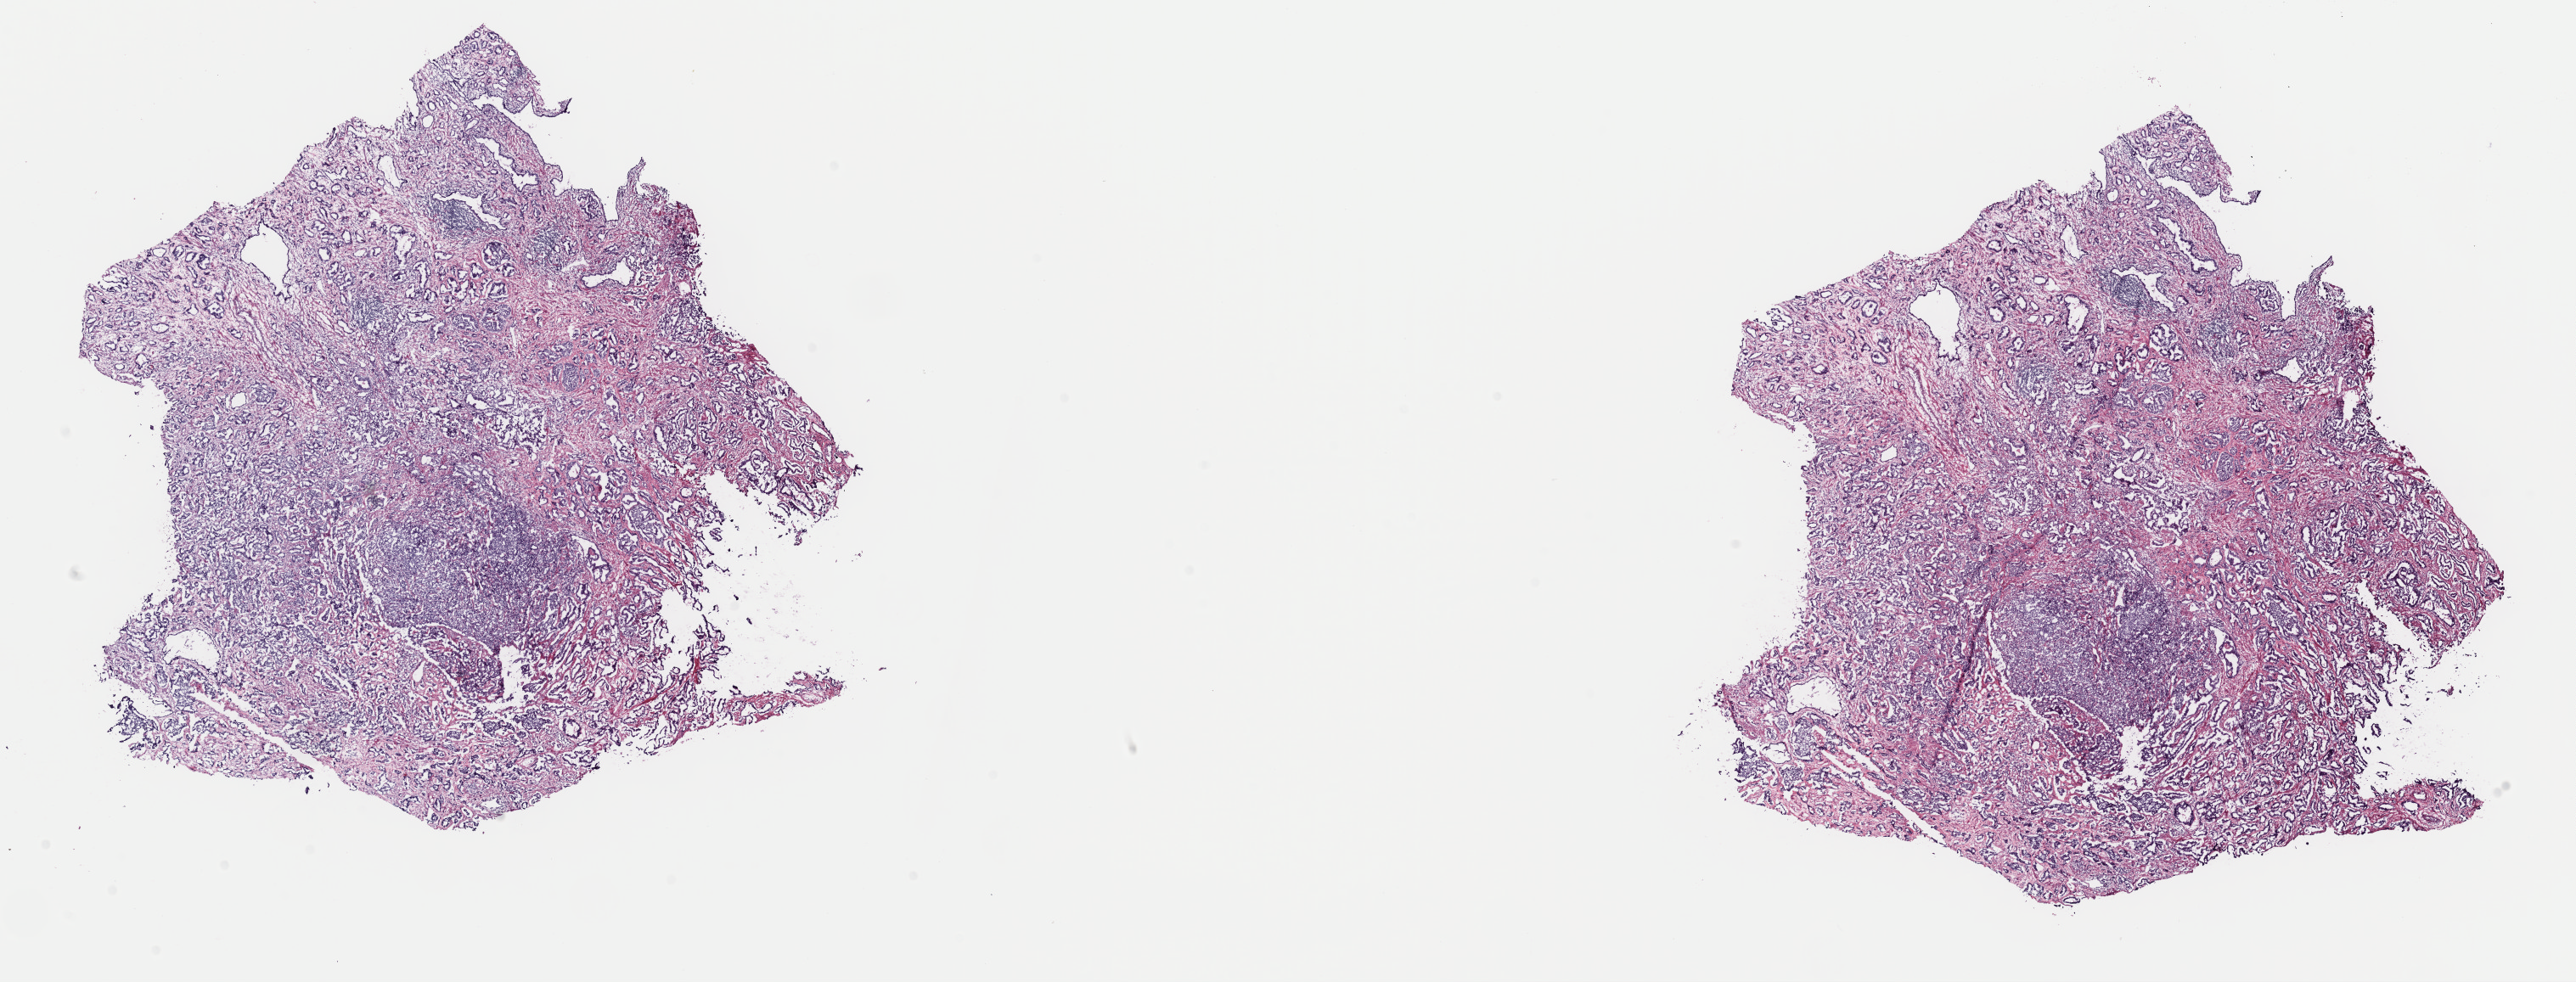
Whole-slide histology image, H&E-stained, low-resolution overview of the scanned area, about 24.0 x 9.1 mm (from a 40x scan); frozen section from the top of the tissue portion; sample: primary tumour, prostate. Male, age 57 years at initial diagnosis. Composition of this section per pathologist review: tumour cells 80%, tumour nuclei 90%.
Diagnosis: Adenocarcinoma, NOS (prostate gland).